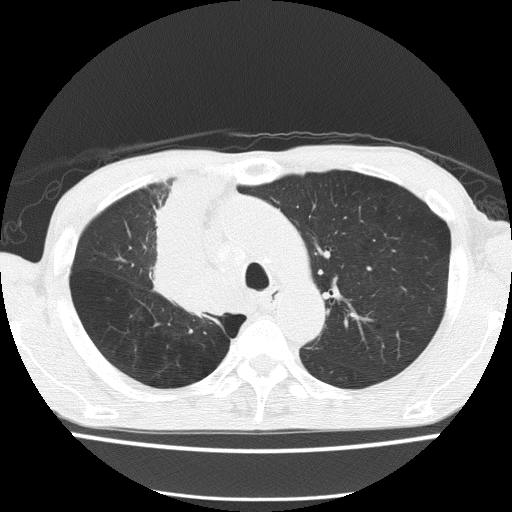
Low-dose screening chest CT, one axial slice; slice 108 of 150 in the series (ordered by position); reconstruction kernel FC51; lung window (W 1500 / L -600 HU); 512 × 512 image matrix, field of view 336 × 336 mm.
Outlined on this slice (expert manual segmentation):
- lesion 1 (tumor, hilum of right lung): bounding box (x1, y1, x2, y2) in pixels: (154, 174, 235, 313)